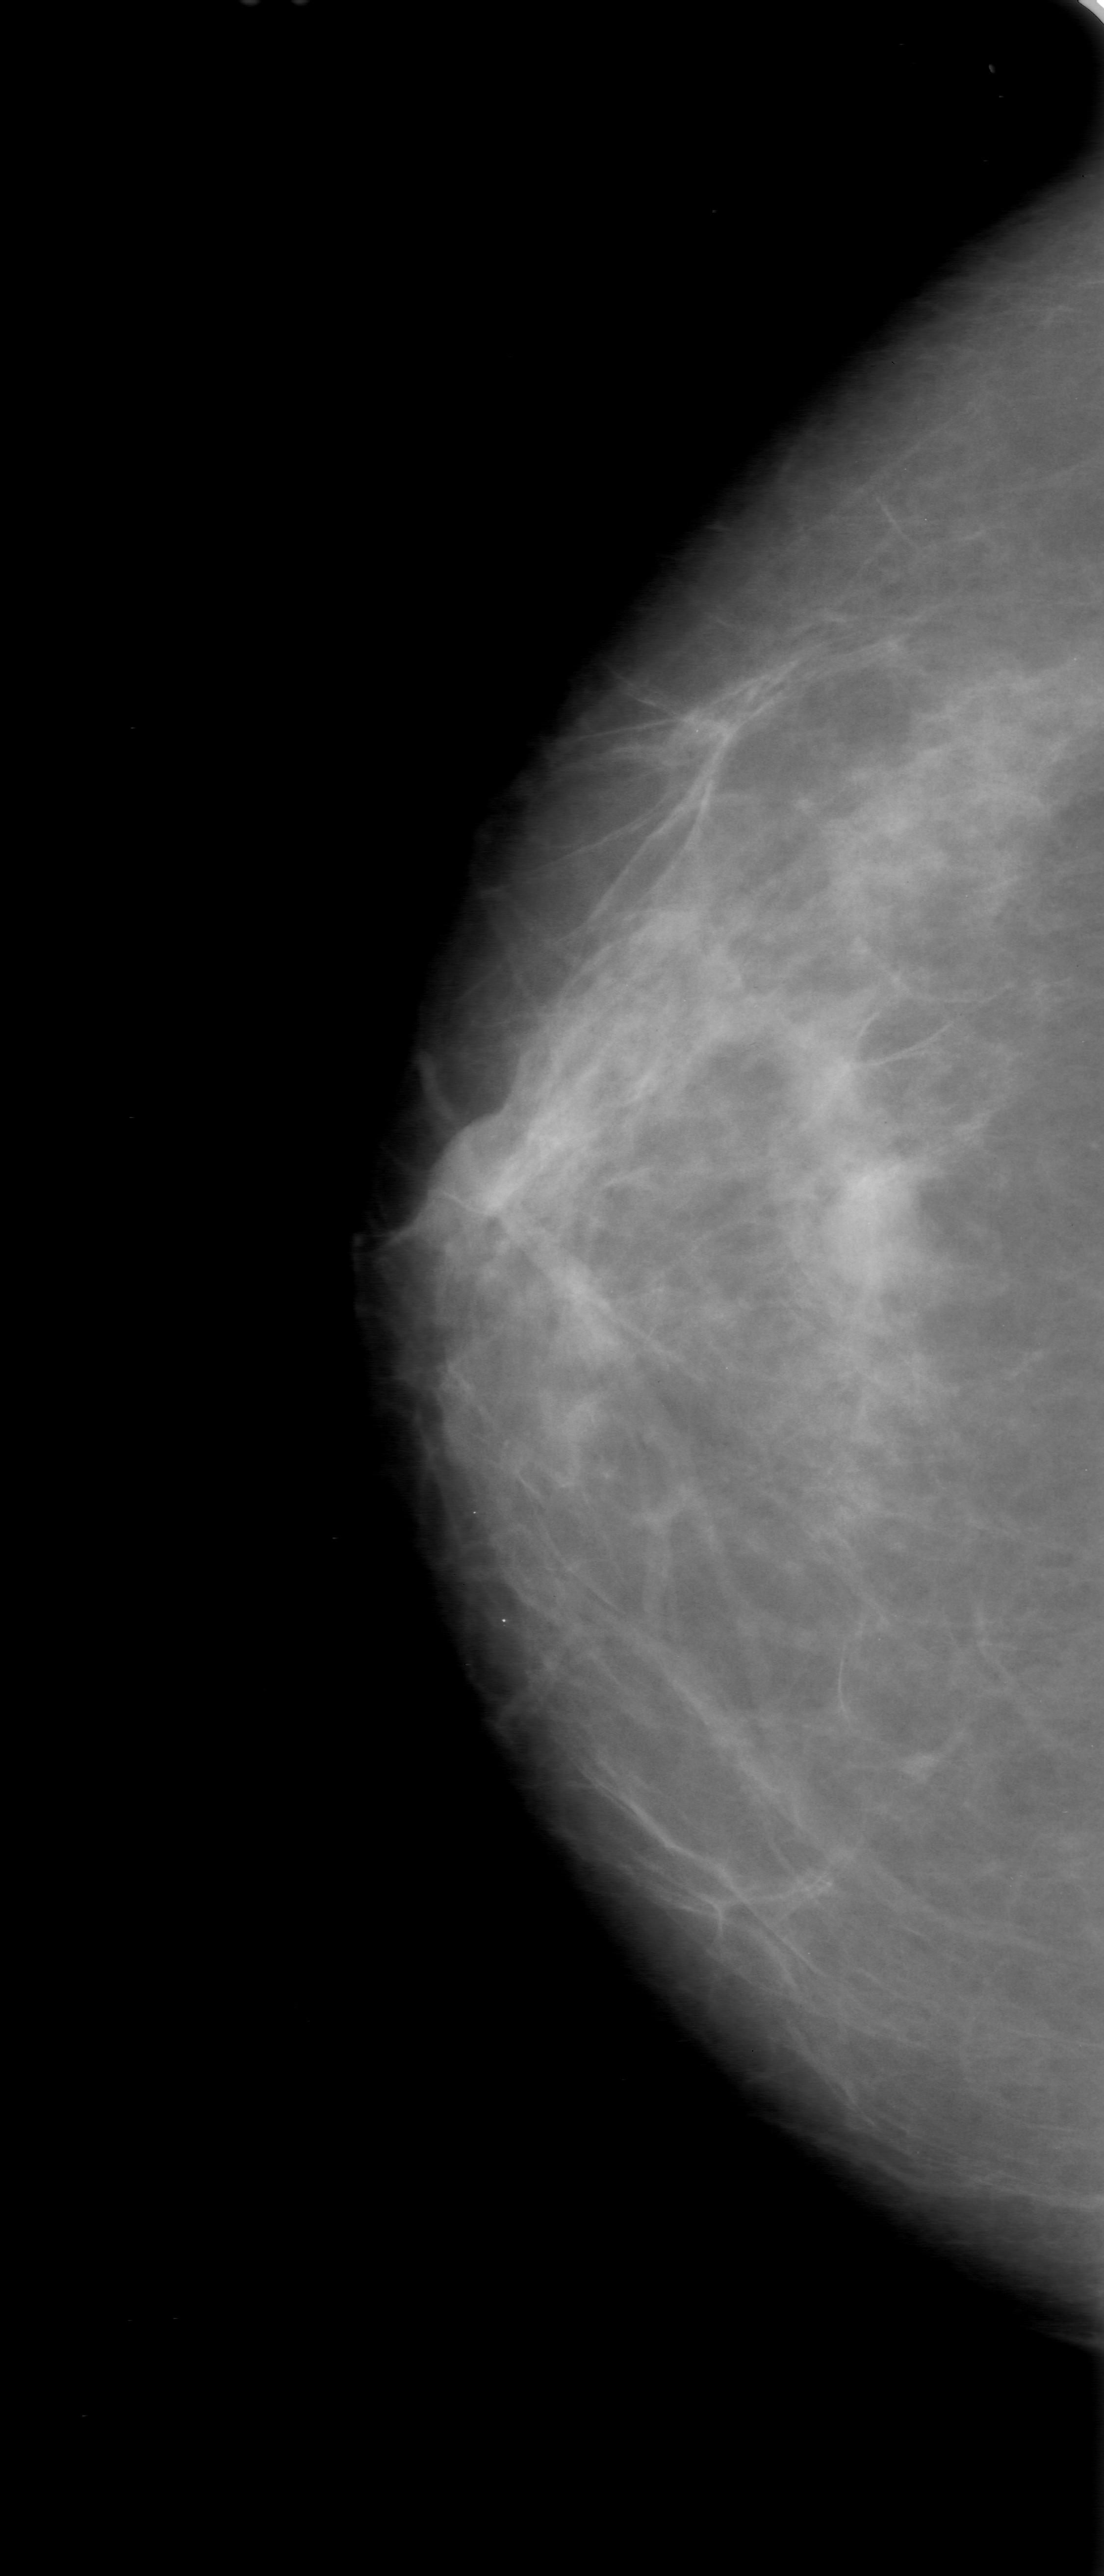
Mammogram (digitized film); right breast; craniocaudal (CC) view; 1104 × 2576 image matrix.
Expert-marked regions of interest on this image (one box per marked abnormality):
- mass, shape oval, margins obscured; BI-RADS assessment category 0; subtlety rating 3 on a 1 (subtle) to 5 (obvious) scale; pathology result (as recorded, not read from the image): benign: box from (x=793, y=1142) to (x=953, y=1322) px